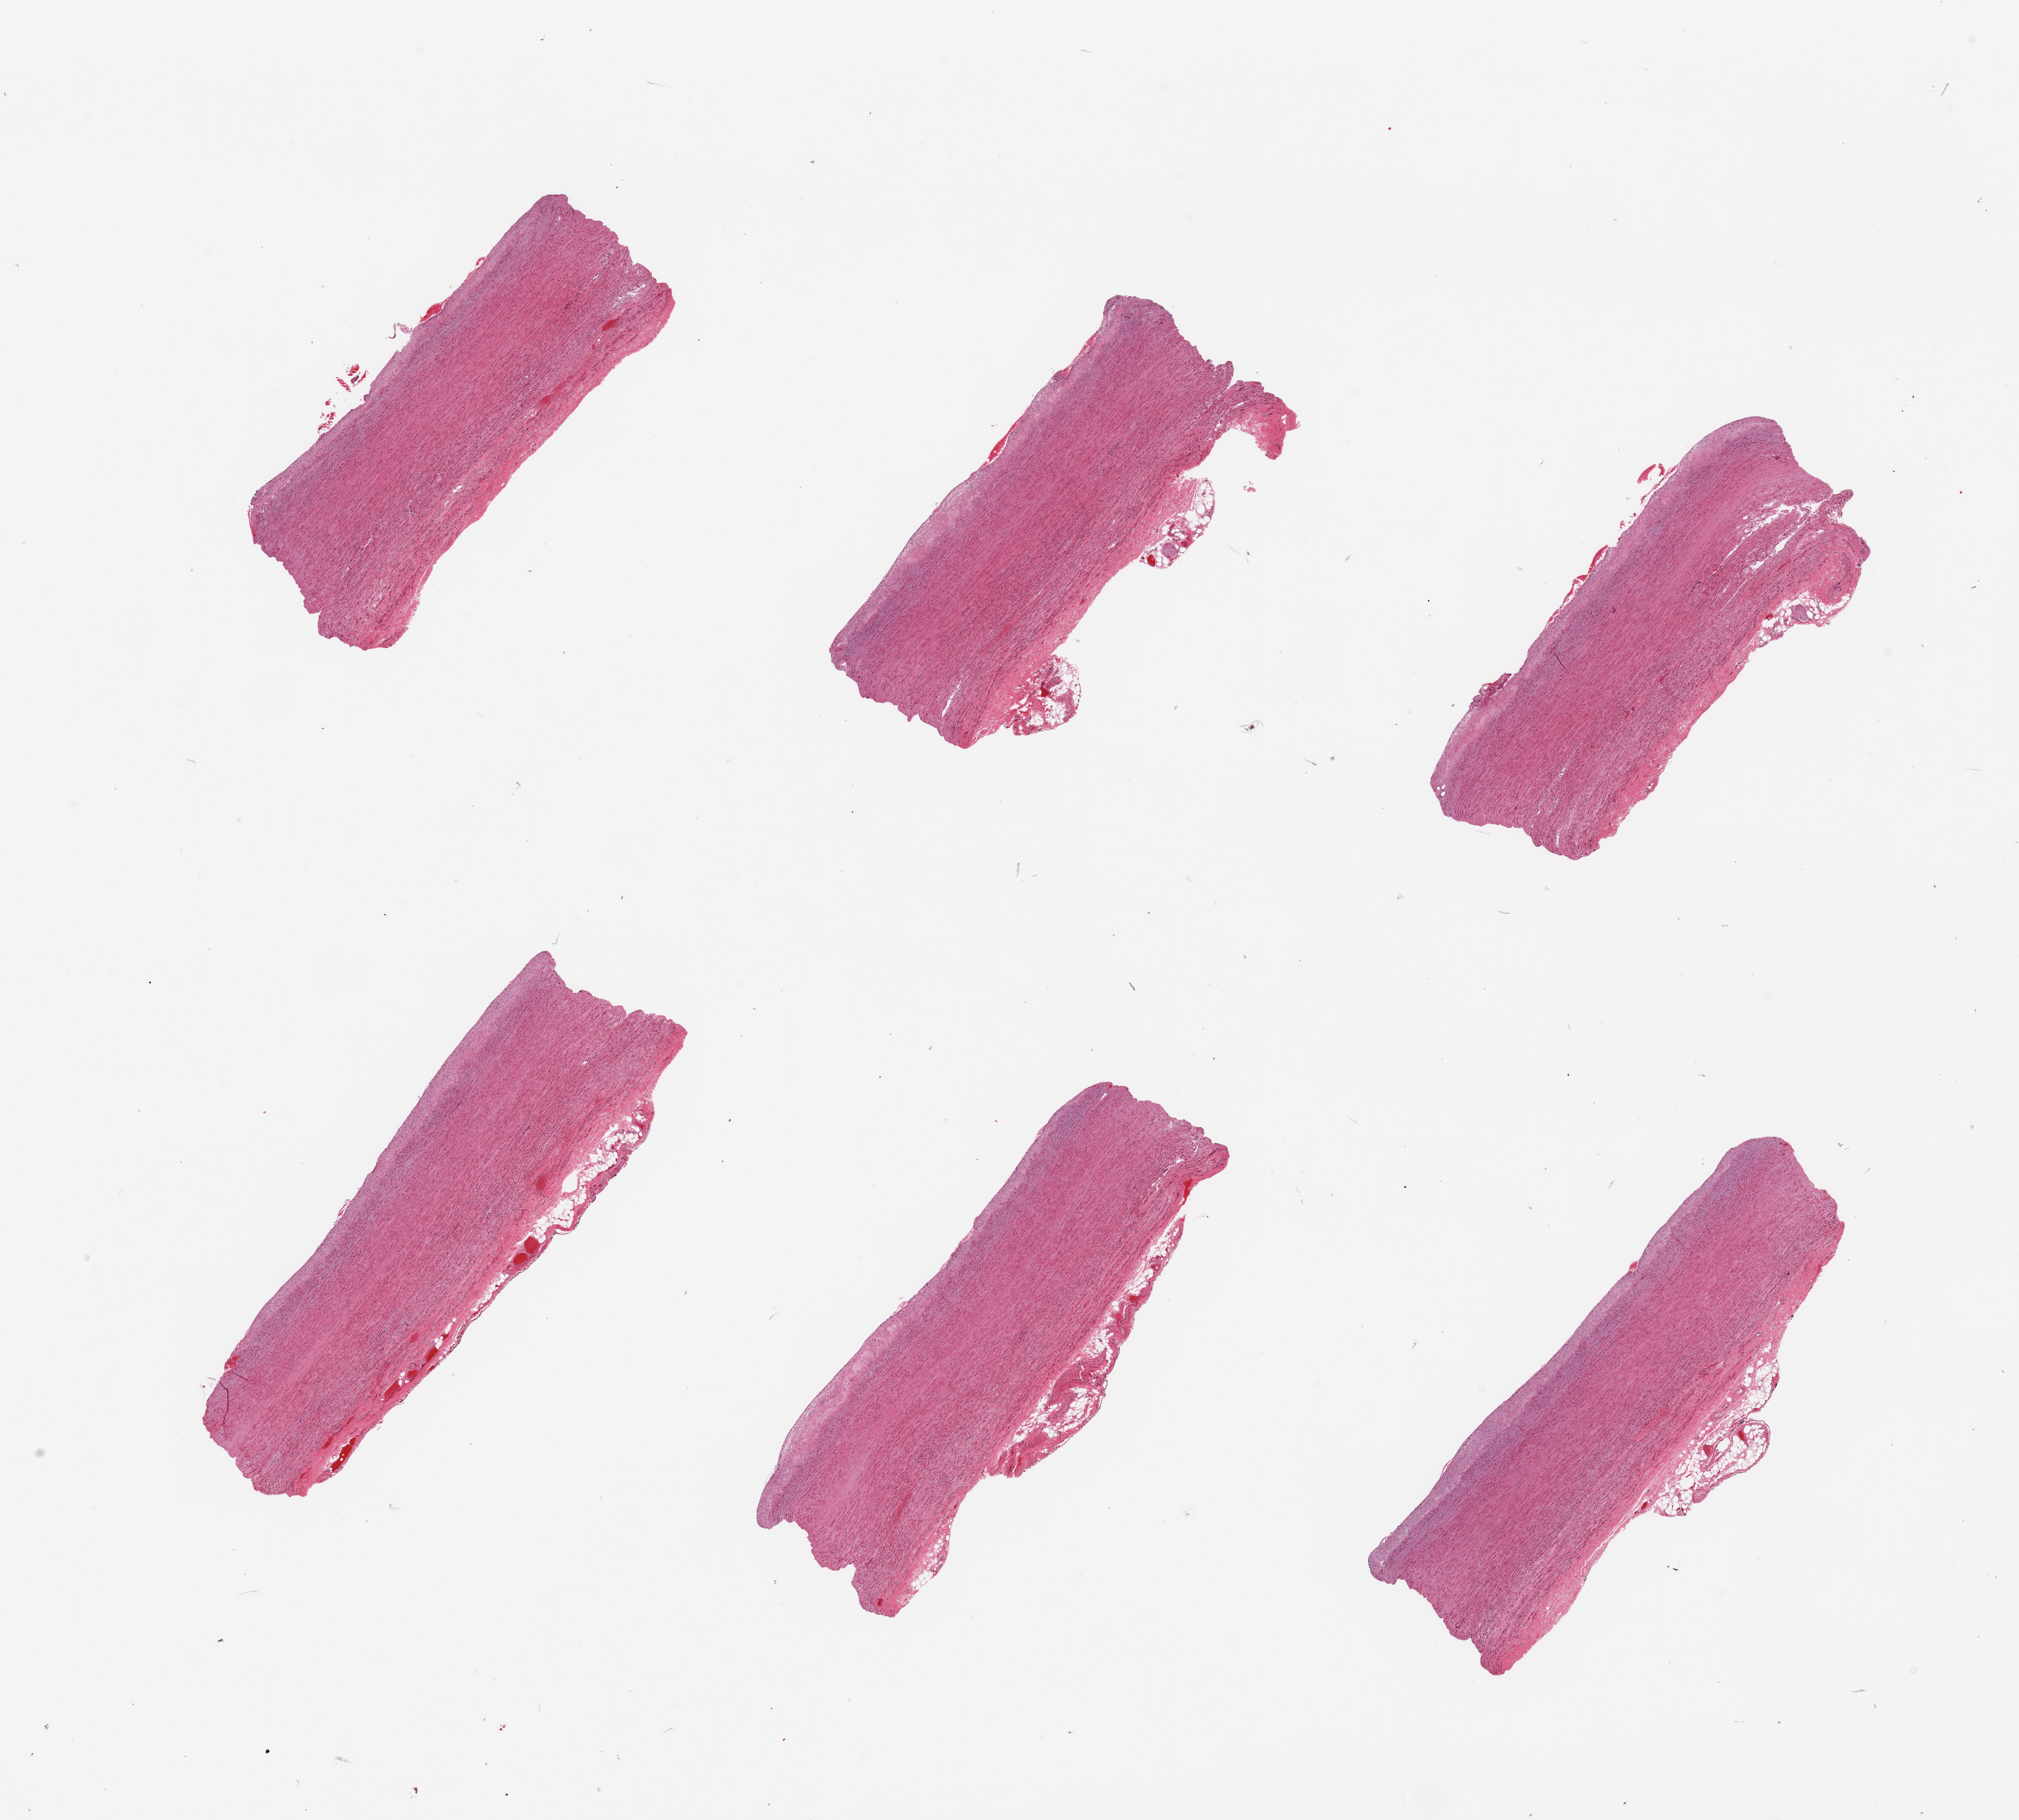
Digitized haematoxylin and eosin-stained section, whole scanned area (about 22.6 x 20.4 mm, slide scanned at 20x) shown as a low-resolution overview; PAXgene-fixed, paraffin-embedded tissue; target tissue: aorta; donor tissue sample. Donor sex: male.
Pathologist's review note for this sample: 6 pieces; flat sclerotic plaque ~0.34 mm thick with focal minute subendothelial red blood cells accumulations; attached up to 0.8mm congested adventitia and fat.